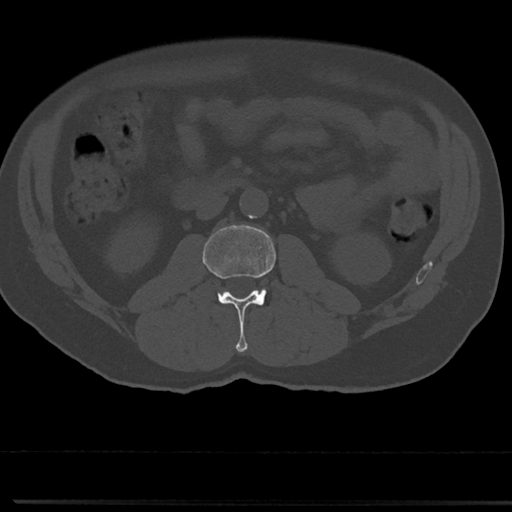
CT including the spine, one axial slice. Position 3 of 817 along the scan axis. Bone window (W 1800 / L 400 HU). 512 × 512 image matrix, field of view 355 × 355 mm. Male patient, age 61 years. From the clinical record (not read from this slice): primary cancer: prostate.
Outlined on this slice (semi-automatically segmented with operator editing):
- L2 vertebra: bounding box [x1, y1, x2, y2] px = [204, 225, 275, 351]